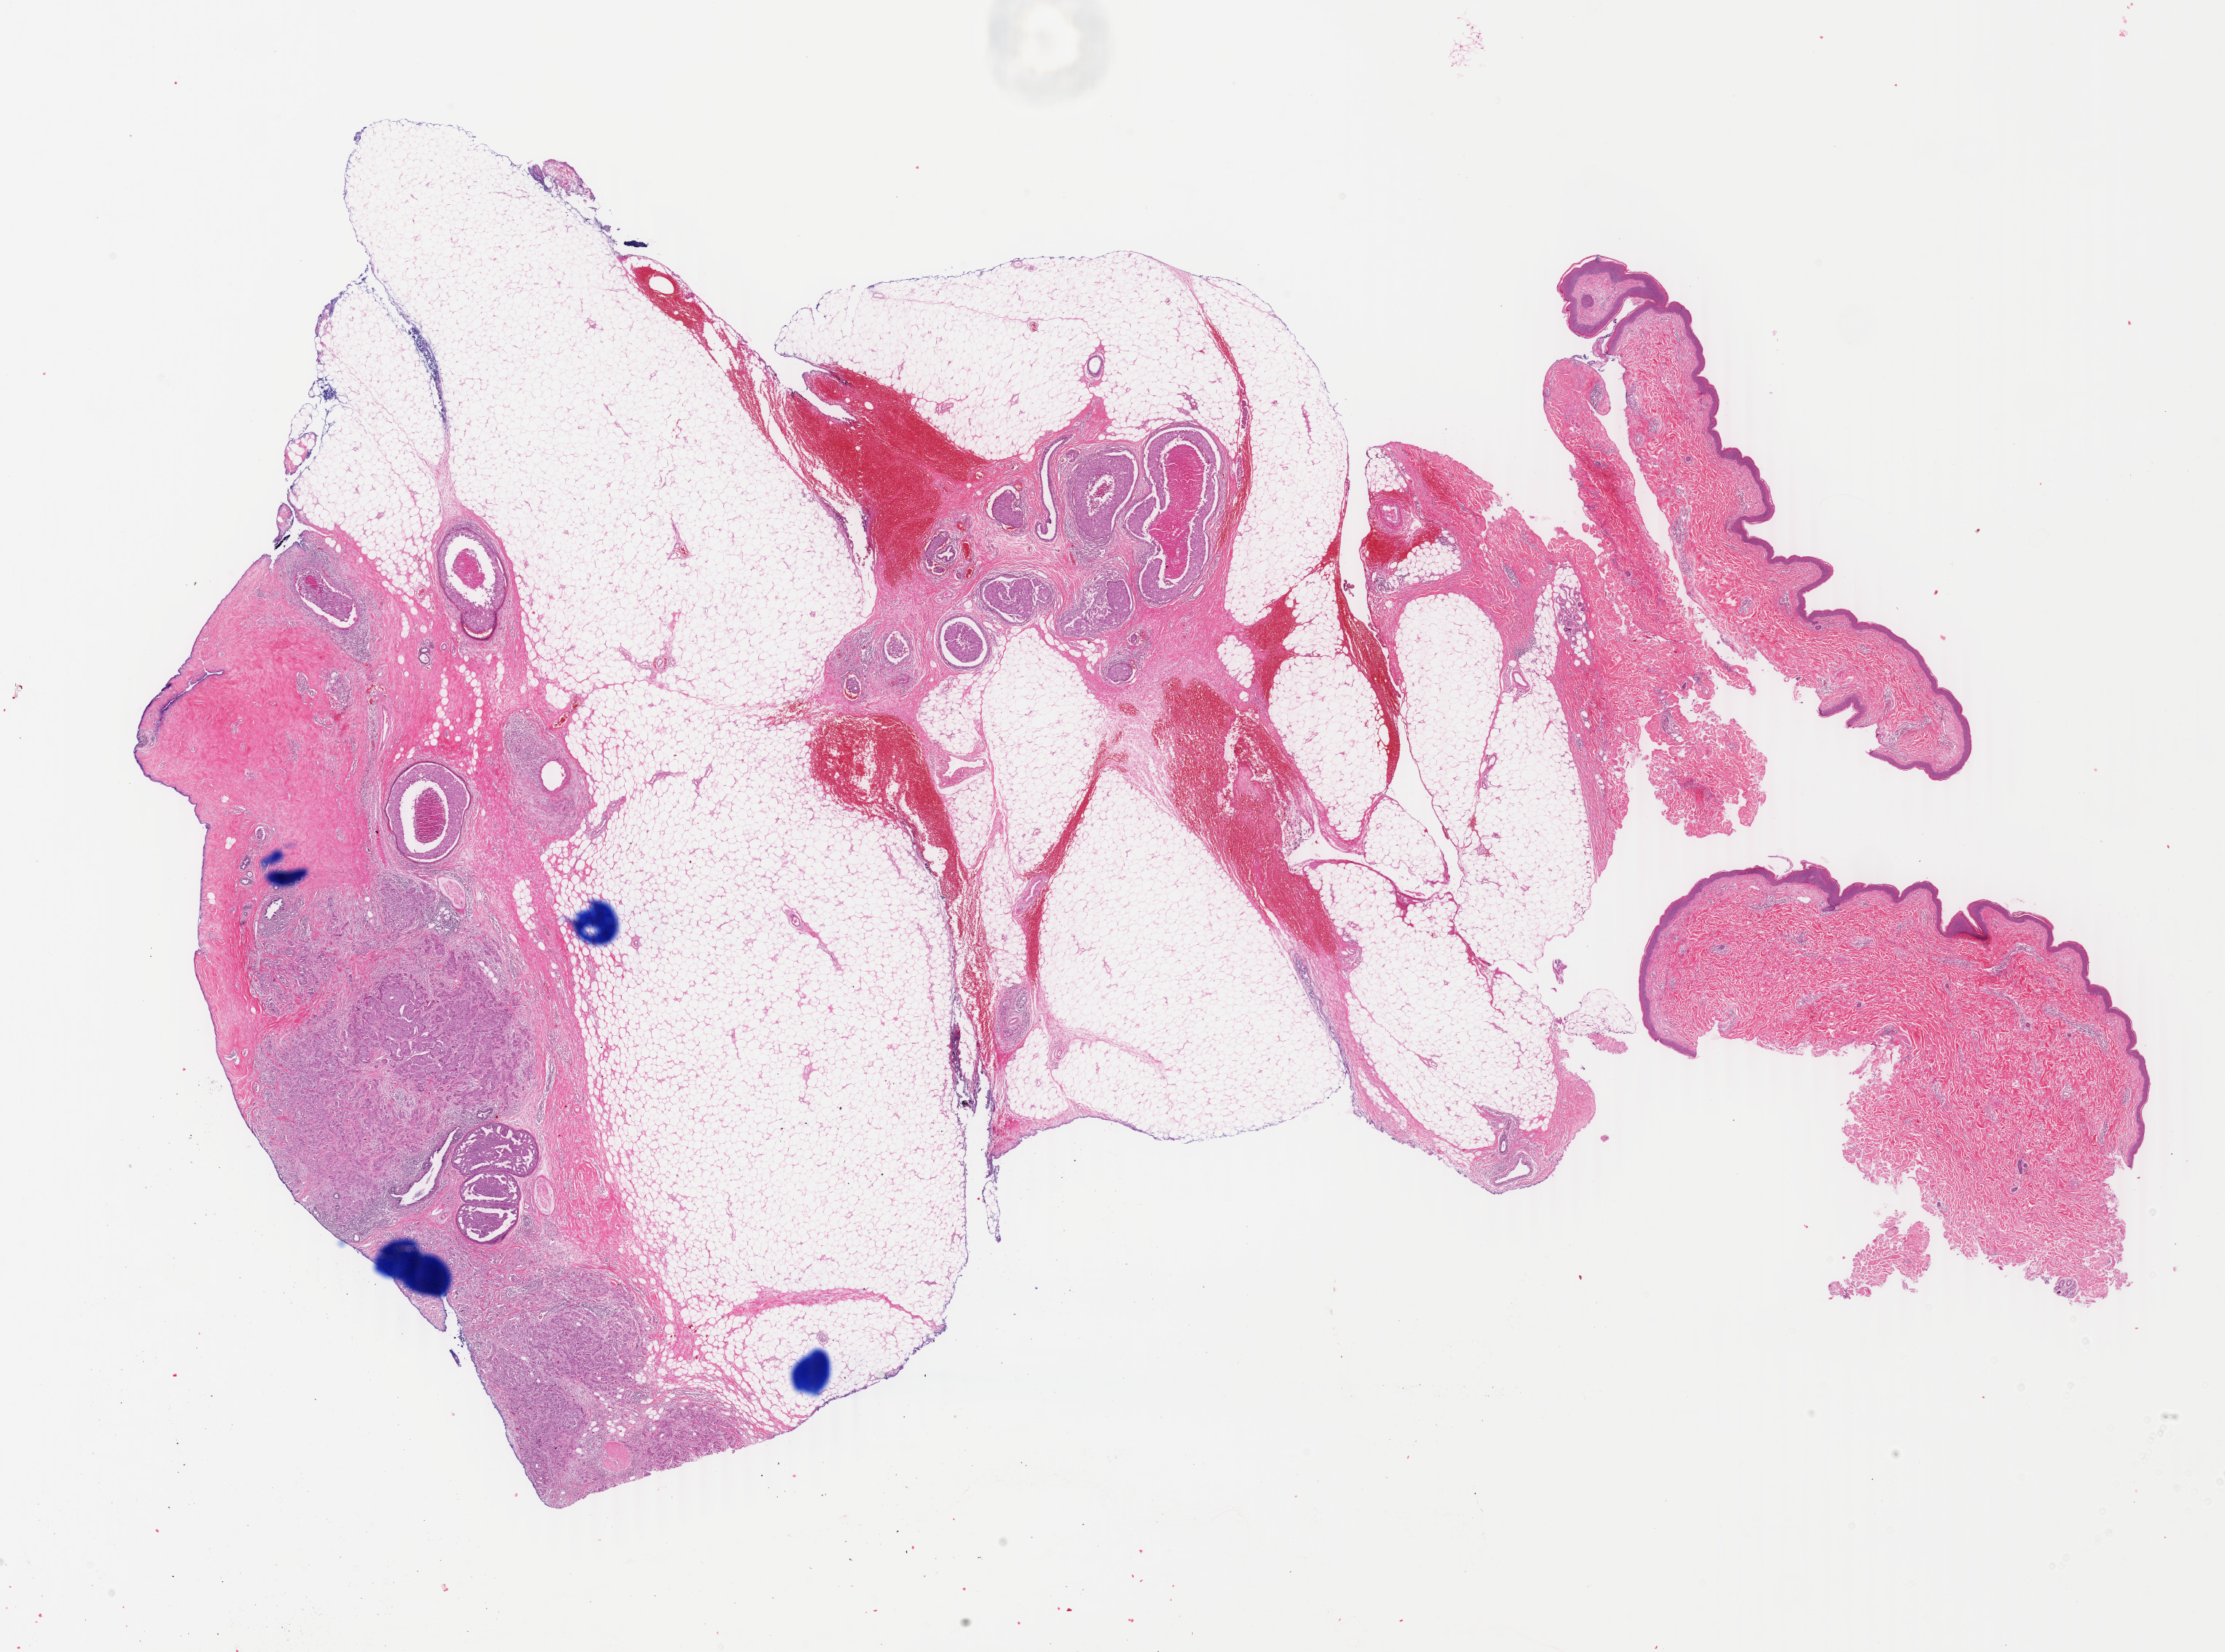
Hematoxylin and eosin (H&E) stained whole-slide image — a low-resolution overview of the entire scanned area, about 24.3 x 18.0 mm (from a 40x scan). Formalin-fixed paraffin-embedded (FFPE) diagnostic section. Sample: primary tumour, breast. Patient: female, age at initial diagnosis 63 years.
* laterality: left
* histologic diagnosis: Infiltrating duct carcinoma, NOS
* lymph nodes positive (case pathology): 1 of 14 examined
* AJCC pathologic stage: IIIB (4th edition)